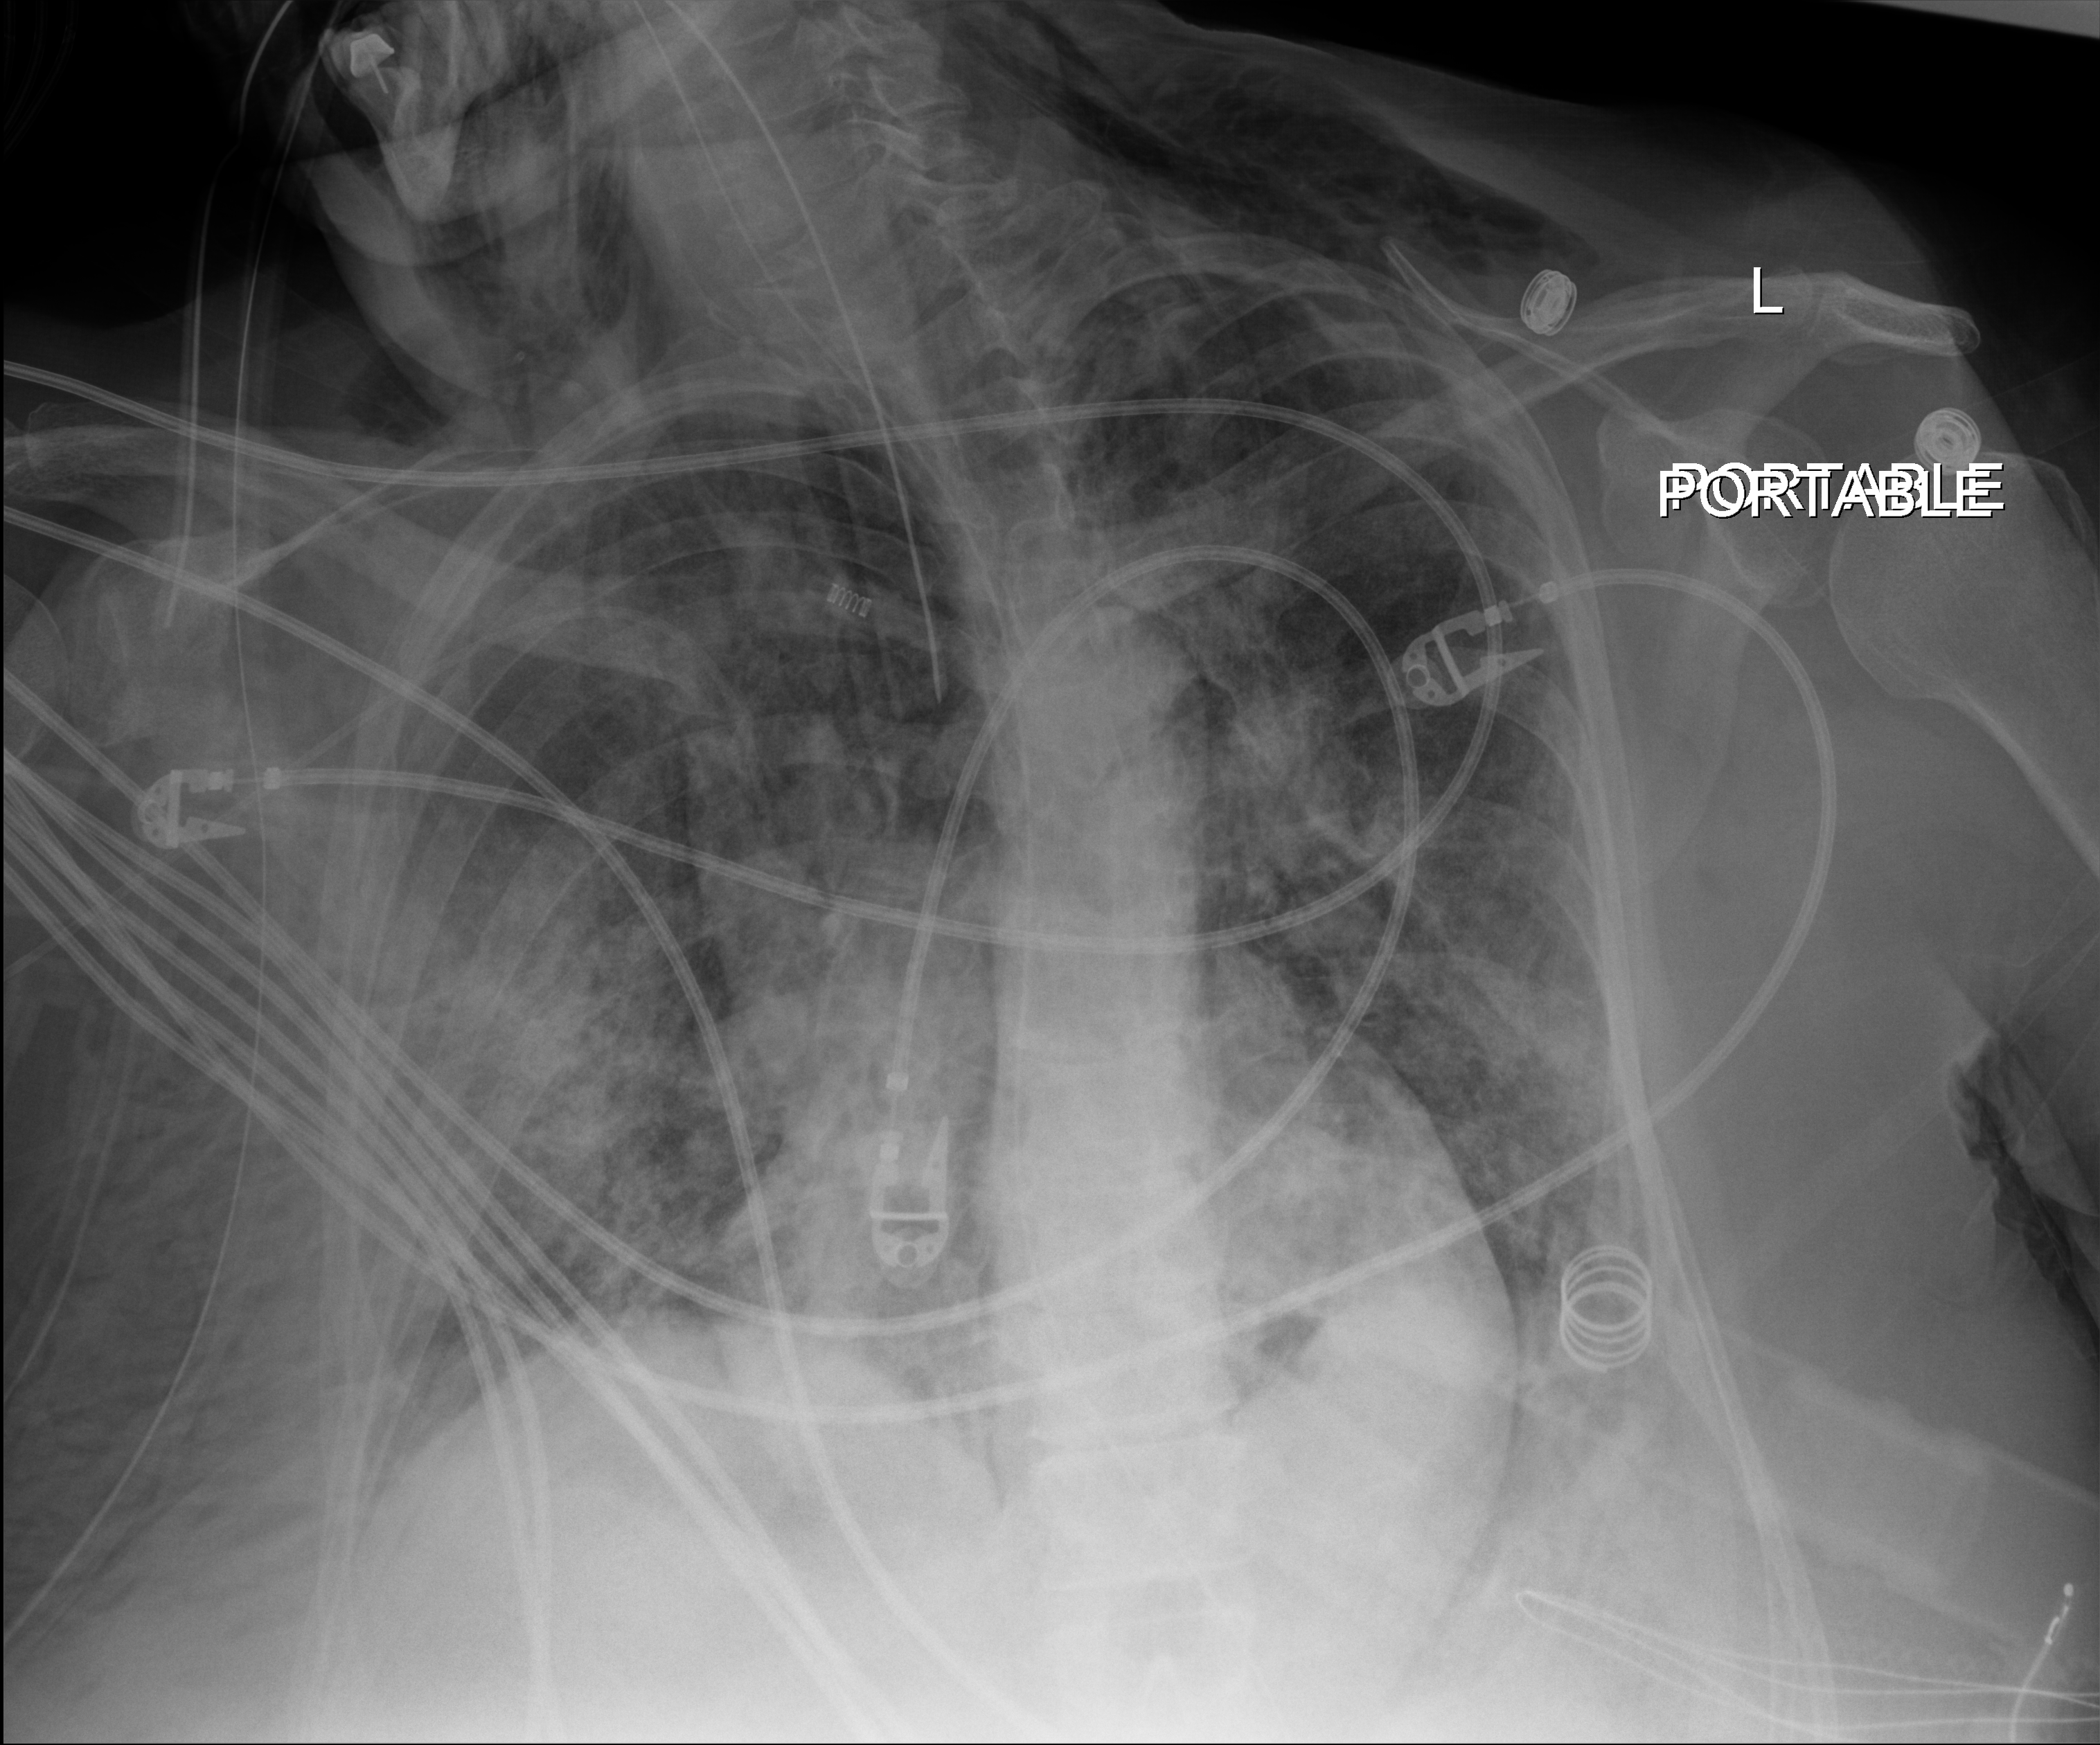
Portable chest radiograph; anteroposterior (AP) projection. Patient hospitalised with COVID-19; female, aged 60–74 years.
From the hospital-stay record, not from the radiograph (when in the stay this image was taken is not recorded): admitted to intensive care during this hospital stay: yes; length of hospital stay: 45 days.